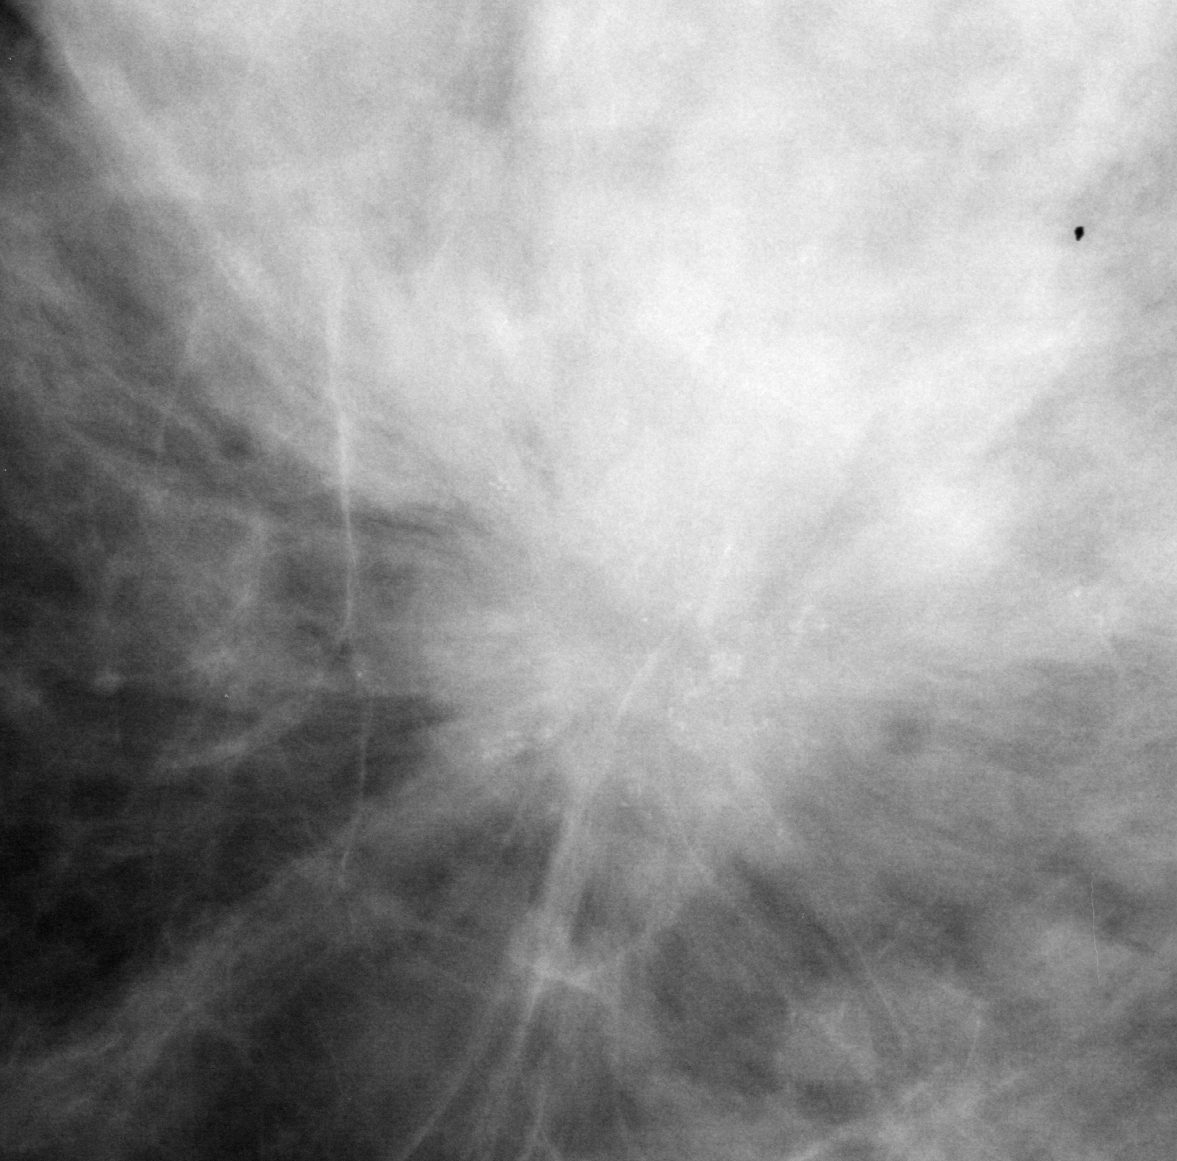
Cropped region of a digitized screen-film mammogram centred on a radiologist-marked abnormality; left breast; CC view.
Finding: calcifications, morphology pleomorphic, distribution clustered; BI-RADS assessment category 5; pathology result (as recorded, not read from the image): malignant.